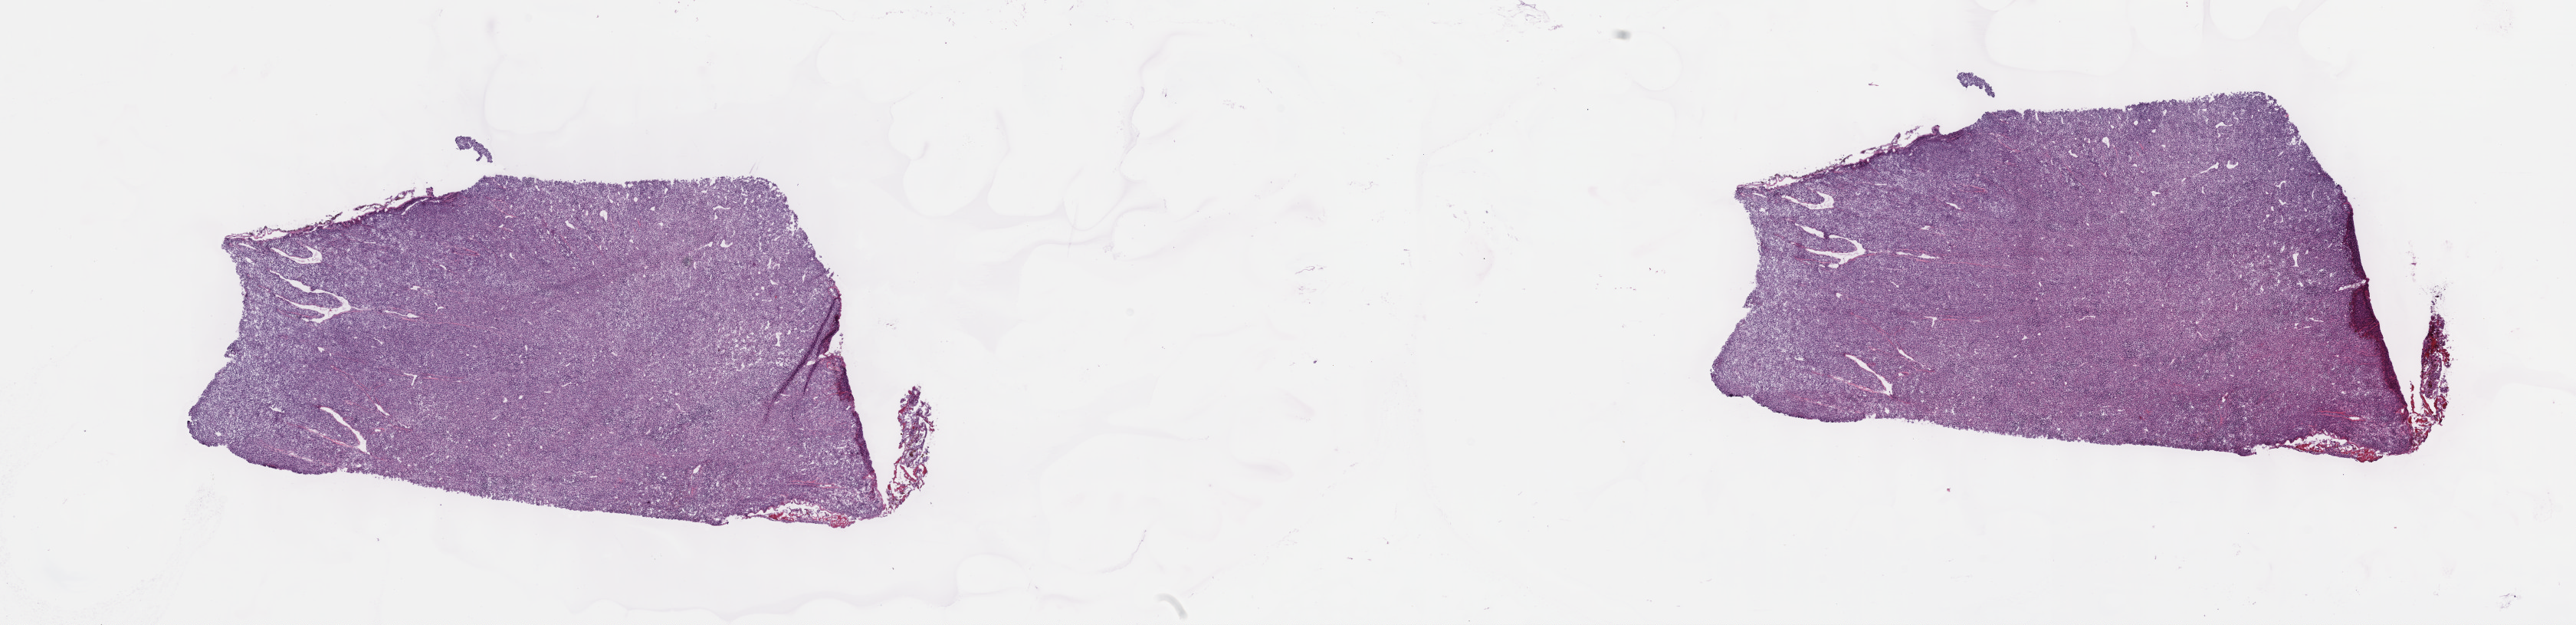
H&E whole-slide image — shown as a low-resolution overview of the whole scanned area (about 27.2 x 6.6 mm); frozen section from the top of the tissue portion; sample: primary tumour, uvea. Male, age 68 years at initial diagnosis. Slide review estimates, as recorded: tumour cells 100%, tumour nuclei 80%, normal cells 0%, stromal cells 0%, necrosis 0%. Infiltration values recorded for this section: lymphocyte infiltration 1%, monocyte infiltration 0%, neutrophil infiltration 0%.
AJCC pathologic stage: IIIB (7th edition). Laterality: right. Pathologic diagnosis: Mixed epithelioid and spindle cell melanoma.